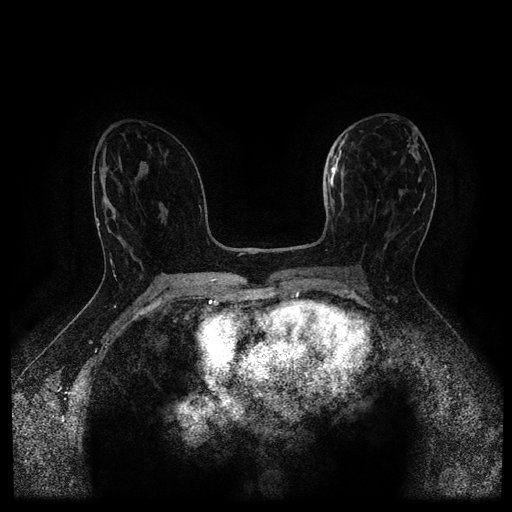
Breast MRI (dynamic contrast-enhanced, multi-phase), one axial slice. Slice 58 of 116 in the series (ordered by position). Dynamic contrast-enhanced series, time point 2 of 5 at this slice position (early post-contrast). 1.5 T. TE 2.7 ms, TR 5.4 ms. 2 mm slice thickness. 512 × 512 image matrix, field of view 340 × 340 mm. Patient: female, 50 years.
Annotated regions visible in this slice (semi-automatic segmentation, software-assisted and operator-edited):
- breast lesion (labelled 'tumour' in the annotation; benign lesions carry a separate 'benign' label): bounding box [x1, y1, x2, y2] px = [327, 143, 344, 192]